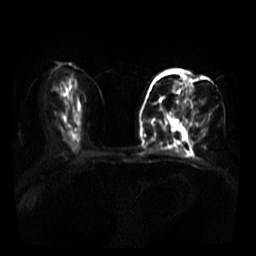
Breast MRI, one axial slice. Slice 18 of 39 in the series (ordered by position). Diffusion-weighted series; image 2 of 4 stored at this slice position (different b-values; order by instance number). 3 T. 5 mm slice thickness. 256 × 256 image matrix, field of view 320 × 320 mm. Female patient.
Annotated regions visible in this slice (manually delineated by an expert):
- tumour on diffusion-weighted imaging: bounding box (x1, y1, x2, y2) in pixels: (158, 83, 192, 102)